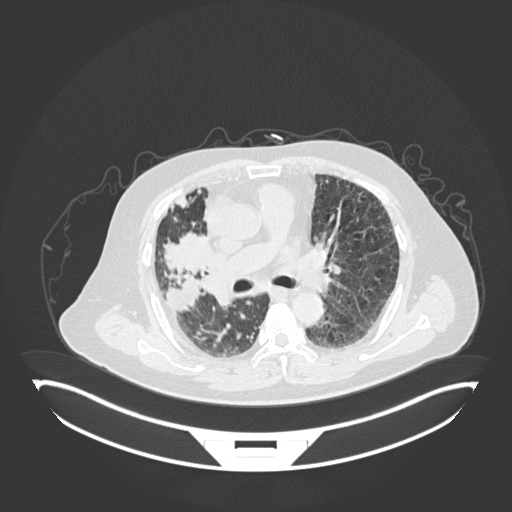
Chest CT, one axial slice. Position 96 of 201 along the scan axis. Reconstruction kernel B30f. Lung window (W 1500 / L -600 HU). 1 mm slice thickness. 512 × 512 image matrix. Male patient, age 69 years. Case-level facts recorded for this patient, not image findings: clinical TNM (as recorded): T4 N3 M1.
Annotated regions visible in this slice (bounding box drawn by a radiologist):
- lung tumour (recorded histology: adenocarcinoma): bounding box [x1, y1, x2, y2] px = [161, 229, 220, 279]